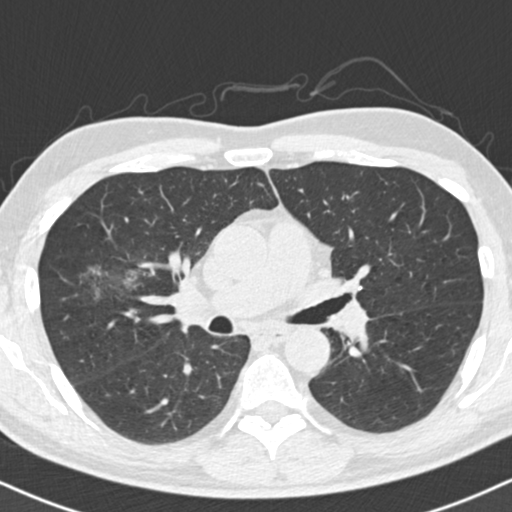
Chest CT (low-dose screening protocol), one axial image, first (baseline) screen, lung window (W 1500 / L -600 HU), standard (soft-tissue) reconstruction kernel (B30f), slice 66 of 154 in the series, 512 × 512 image matrix. Male participant, aged 56 years at enrolment. Former smoker at enrolment.
• Lesion marked by an expert reader, box from (x=61, y=251) to (x=153, y=318) px.
• Screening reader's record for this exam: no non-calcified nodule ≥4 mm recorded.
• Lung cancer was diagnosed 392 days after this screen: bronchiolo-alveolar adenocarcinoma, NOS, right upper lobe, well differentiated (G1), stage IIB (AJCC 6th edition), 30 mm at pathology.